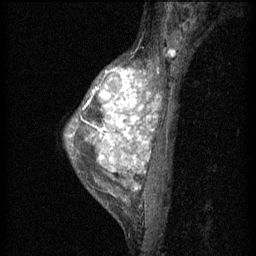
Breast MRI (dynamic contrast-enhanced), one sagittal slice; slice 40 of 60 in the series (ordered by position); 3 images stored at this slice position (order not interpretable as contrast timing); 1.5 T; TE 4.2 ms, TR 11 ms; 256 × 256 image matrix, field of view 180 × 180 mm. Patient: female, 40 years.
Annotated regions visible in this slice (semi-automatic segmentation, software-assisted and operator-edited):
- analysis volume of interest (the breast-tissue region the enhancement analysis was run in; not a lesion): bounding box (x1, y1, x2, y2) in pixels: (65, 48, 172, 203)
- tumour enhancement mask (voxels above the 70 % enhancement threshold inside the analysis volume of interest): (82, 68, 160, 191)